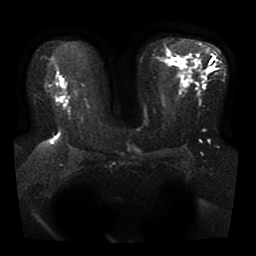
Breast MRI, one axial slice. Slice 20 of 41 in the series (ordered by position). Diffusion-weighted series; image 2 of 4 stored at this slice position (different b-values; order by instance number). 1.5 T. 5 mm slice thickness. 256 × 256 image matrix, field of view 330 × 330 mm. Female patient.
Outlined on this slice (outlined manually by an expert reader):
- tumour on diffusion-weighted imaging: bounding box <59,94,67,100> (left, top, right, bottom; pixels)